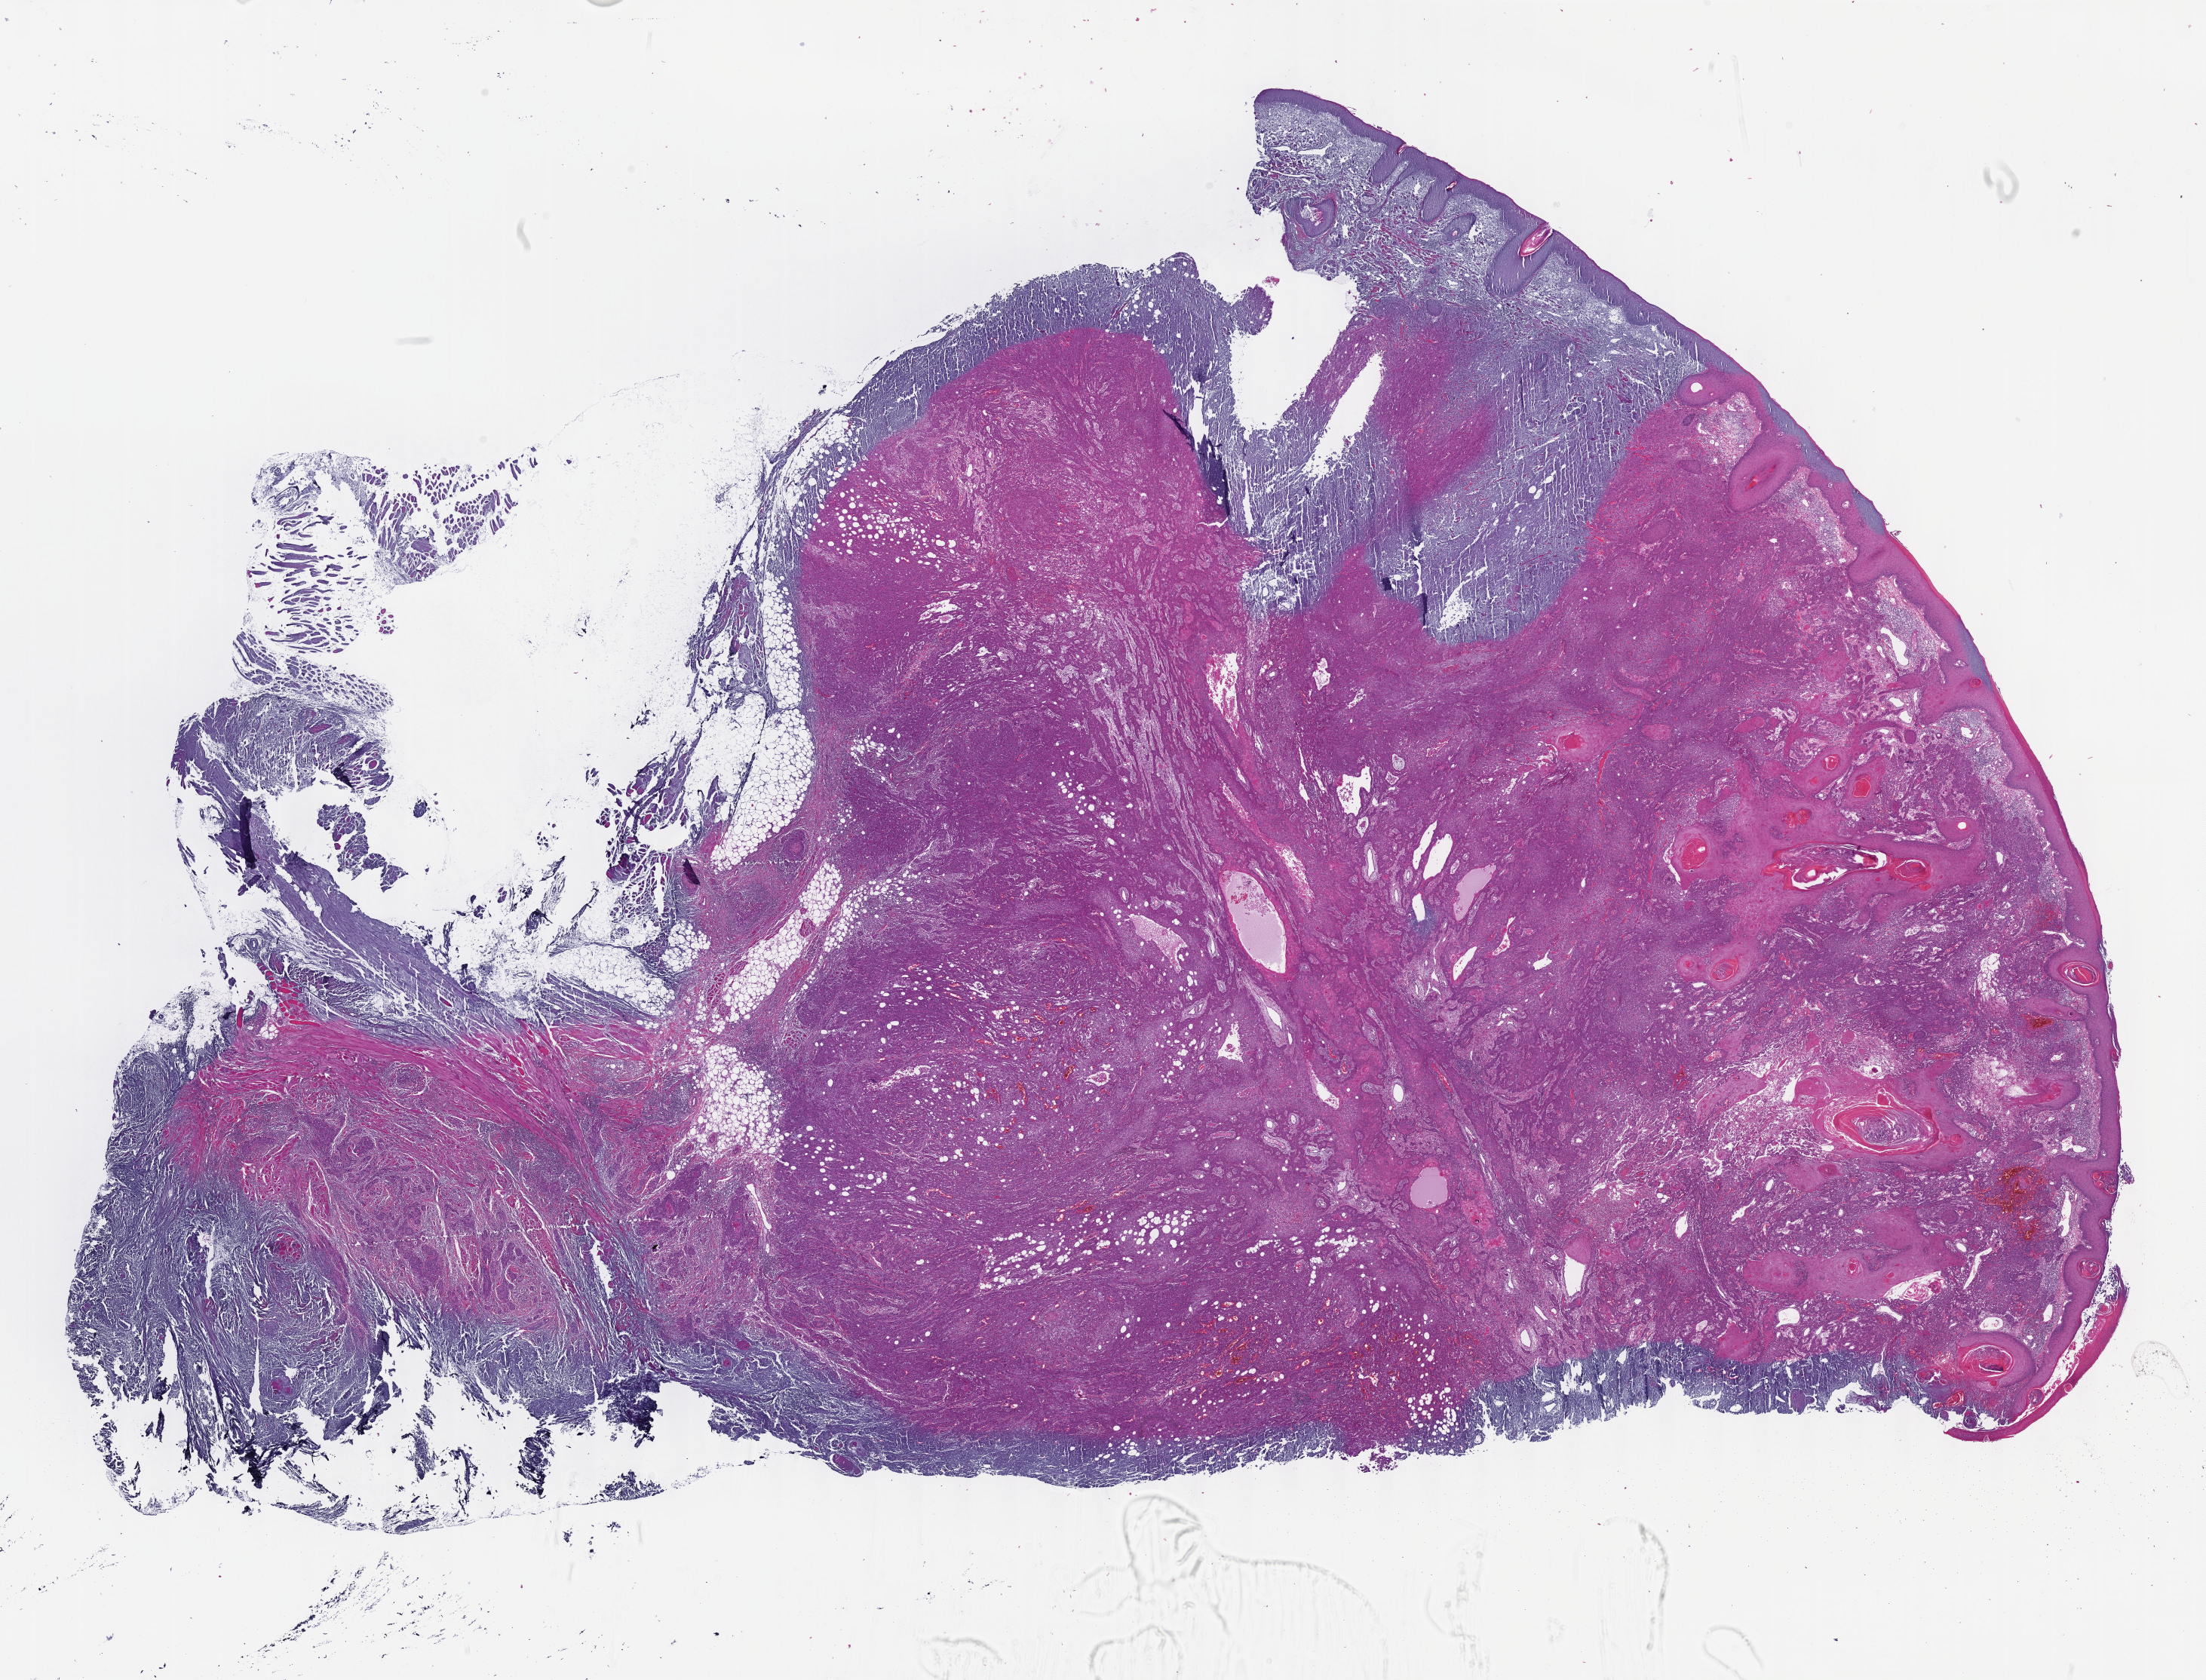
Whole-slide histology image, H&E, whole scanned area (about 23.6 x 18.0 mm, slide scanned at 40x) shown as a low-resolution overview, formalin-fixed paraffin-embedded (FFPE) diagnostic section, head and neck, primary tumour sample. Female, age 48 years at initial diagnosis. Histologic grade: GX (grade cannot be assessed).
* AJCC pathologic stage: IVA (7th edition)
* diagnosis: Squamous cell carcinoma, NOS (overlapping lesion of lip, oral cavity and pharynx)